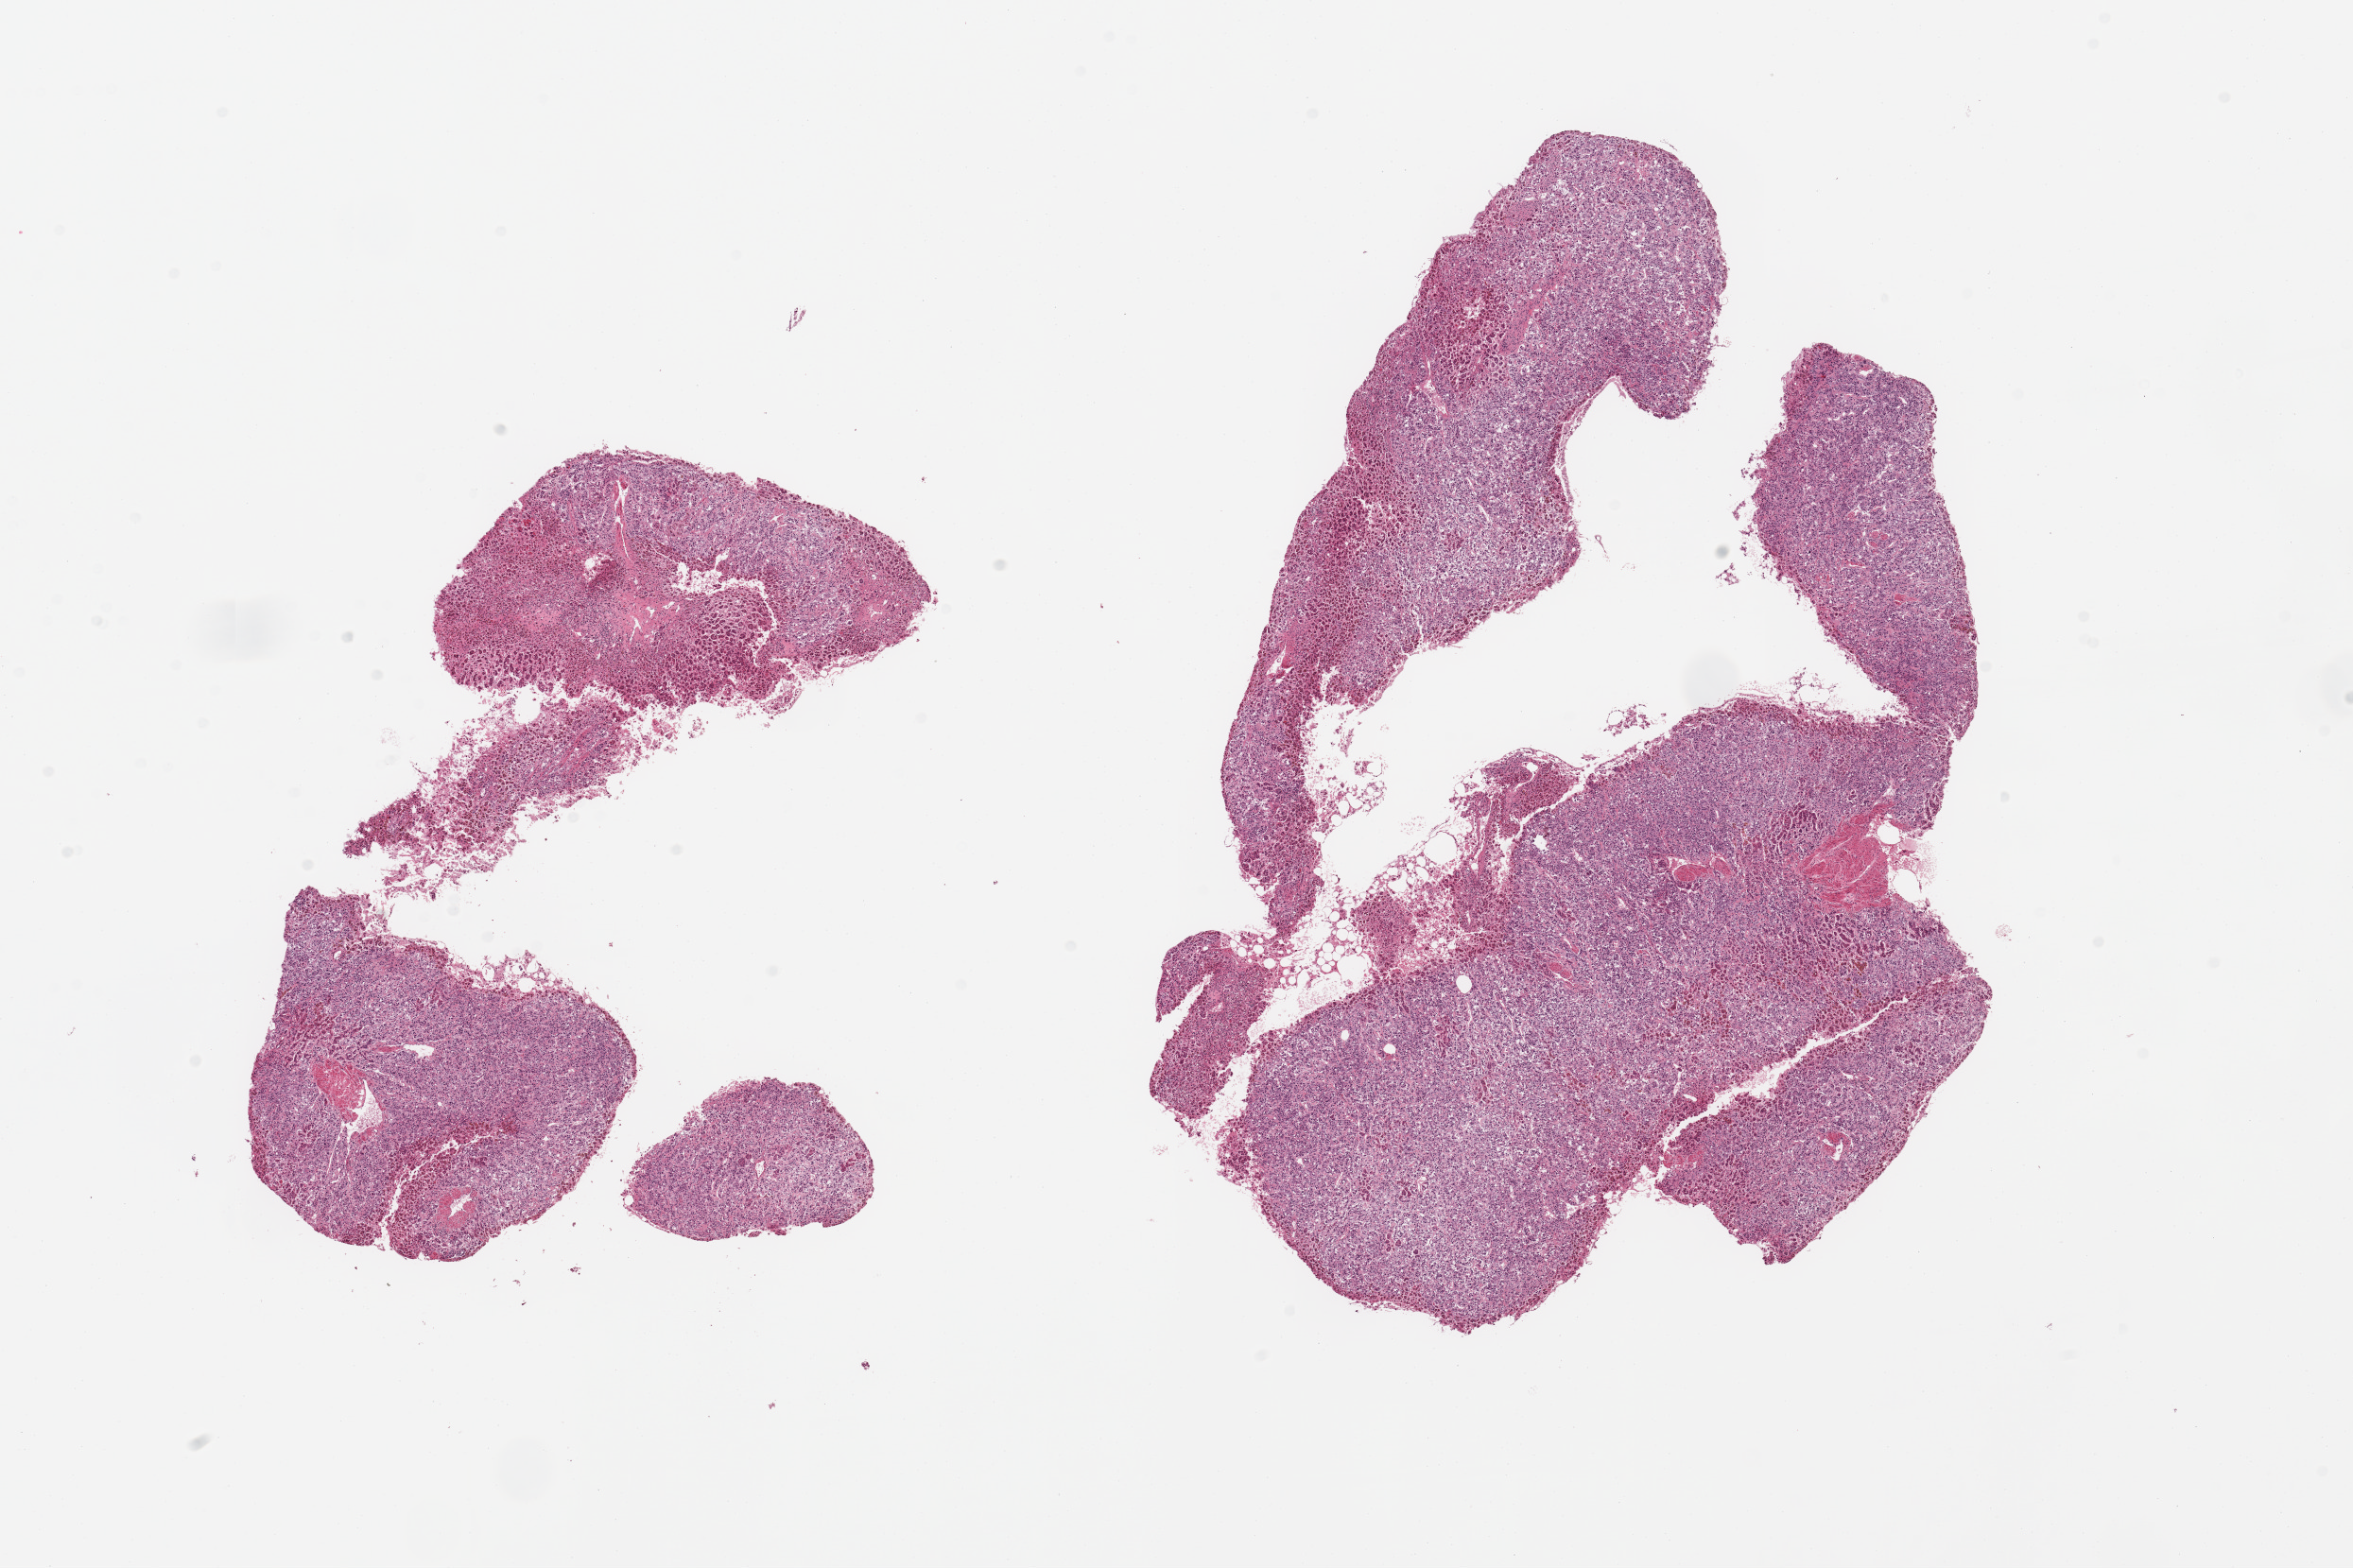
Whole-slide image, haematoxylin and eosin stain — a low-resolution overview of the entire scanned area, about 19.7 x 13.1 mm (from a 20x scan). PAXgene-fixed, paraffin-embedded tissue. Section of adrenal gland (target tissue). Donor tissue sample. Donor sex: male.
* review note (as recorded): 2 pieces (fragmented); medullary hyperplasia